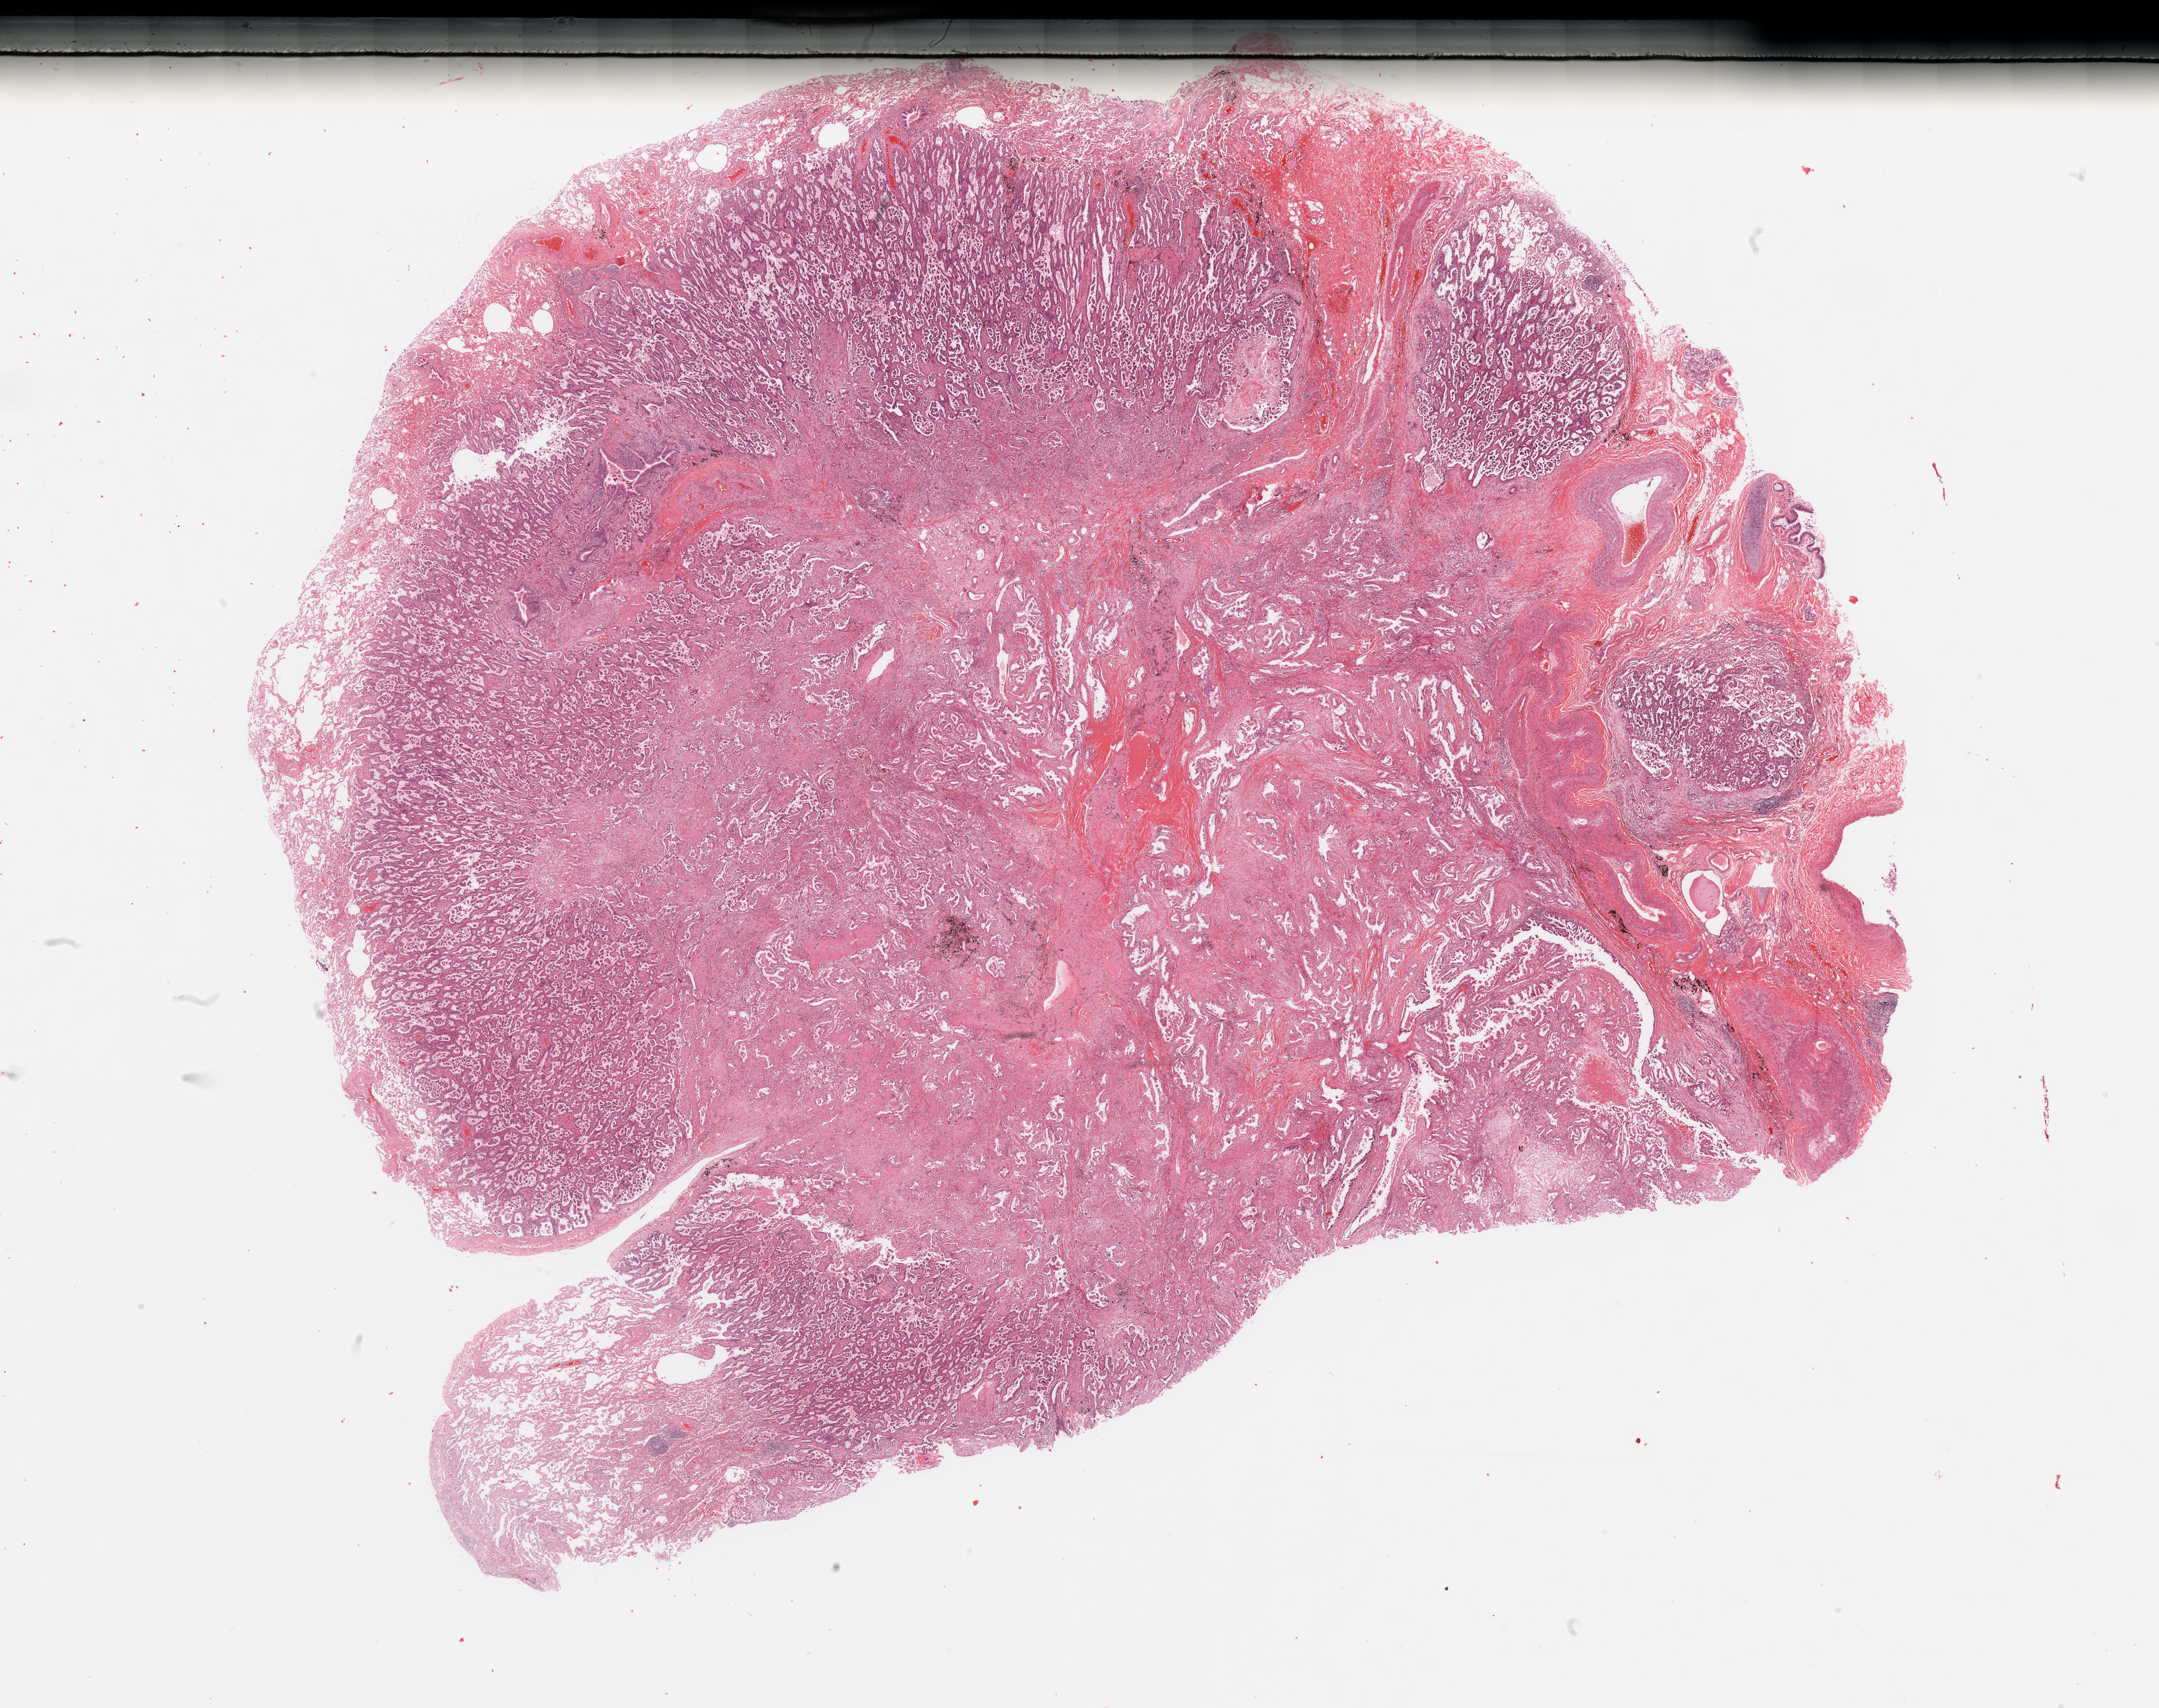
Whole-slide histology image, H&E, whole scanned area (about 28.5 x 22.6 mm, from a 20x scan) shown as a low-resolution overview, tumour tissue sample, sampled site: lung. Patient: female, age 60 years. Histologic grade: G2 (moderately differentiated). Slide review estimates, as recorded: tumour nuclei 75%, necrosis 2%.
AJCC pathologic stage: IB. Histologic diagnosis: Adenocarcinoma, NOS.